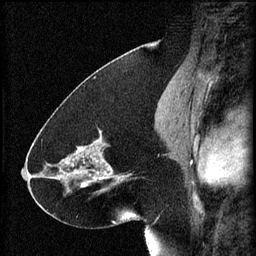
Breast MRI (dynamic contrast-enhanced), one sagittal slice. Position 32 of 60 along the scan axis. 3 images stored at this slice position (order not interpretable as contrast timing). 1.5 T. TE 4.2 ms, TR 8.2 ms. 2 mm slice thickness. 256 × 256 image matrix. Female patient, age 41 years.
Annotated regions visible in this slice (semi-automatic segmentation, software-assisted and operator-edited):
- analysis volume of interest (the breast-tissue region the enhancement analysis was run in; not a lesion): bounding box <72,128,134,195> (left, top, right, bottom; pixels)
- tumour enhancement mask (voxels above the 70 % enhancement threshold inside the analysis volume of interest): <72,132,126,187>